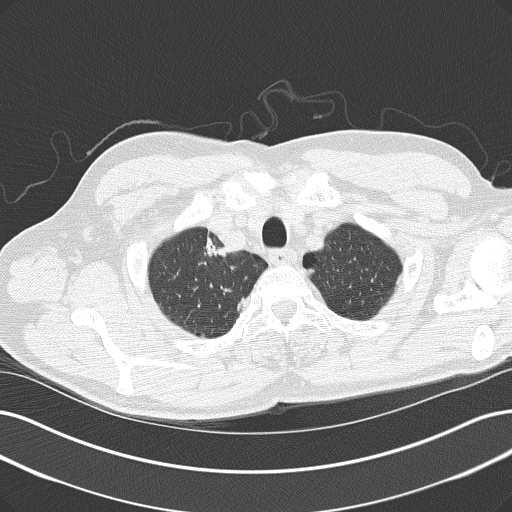
Low-dose screening chest CT, axial slice, baseline screening round, lung window (W 1500 / L -600 HU), 2 mm slice thickness, slice 22 of 152 in the series. Male participant, aged 61 years at enrolment. Current smoker at enrolment.
• Expert-annotated lung lesion, bounding box (x1, y1, x2, y2) in pixels: (193, 228, 245, 273).
• The screening reader recorded 2 non-calcified nodules or masses ≥4 mm on this exam (right upper lobe, right upper lobe); which of them this box marks is not recorded.
• Official screen result: positive, change unspecified: nodule(s) >= 4 mm or enlarging nodule(s), mass(es), or other non-specific abnormalities suspicious for lung cancer.
• Participant outcome: lung cancer diagnosed 54 days after this screen — adenocarcinoma, NOS, right upper lobe, poorly differentiated (G3), stage IIIB (AJCC 6th edition).